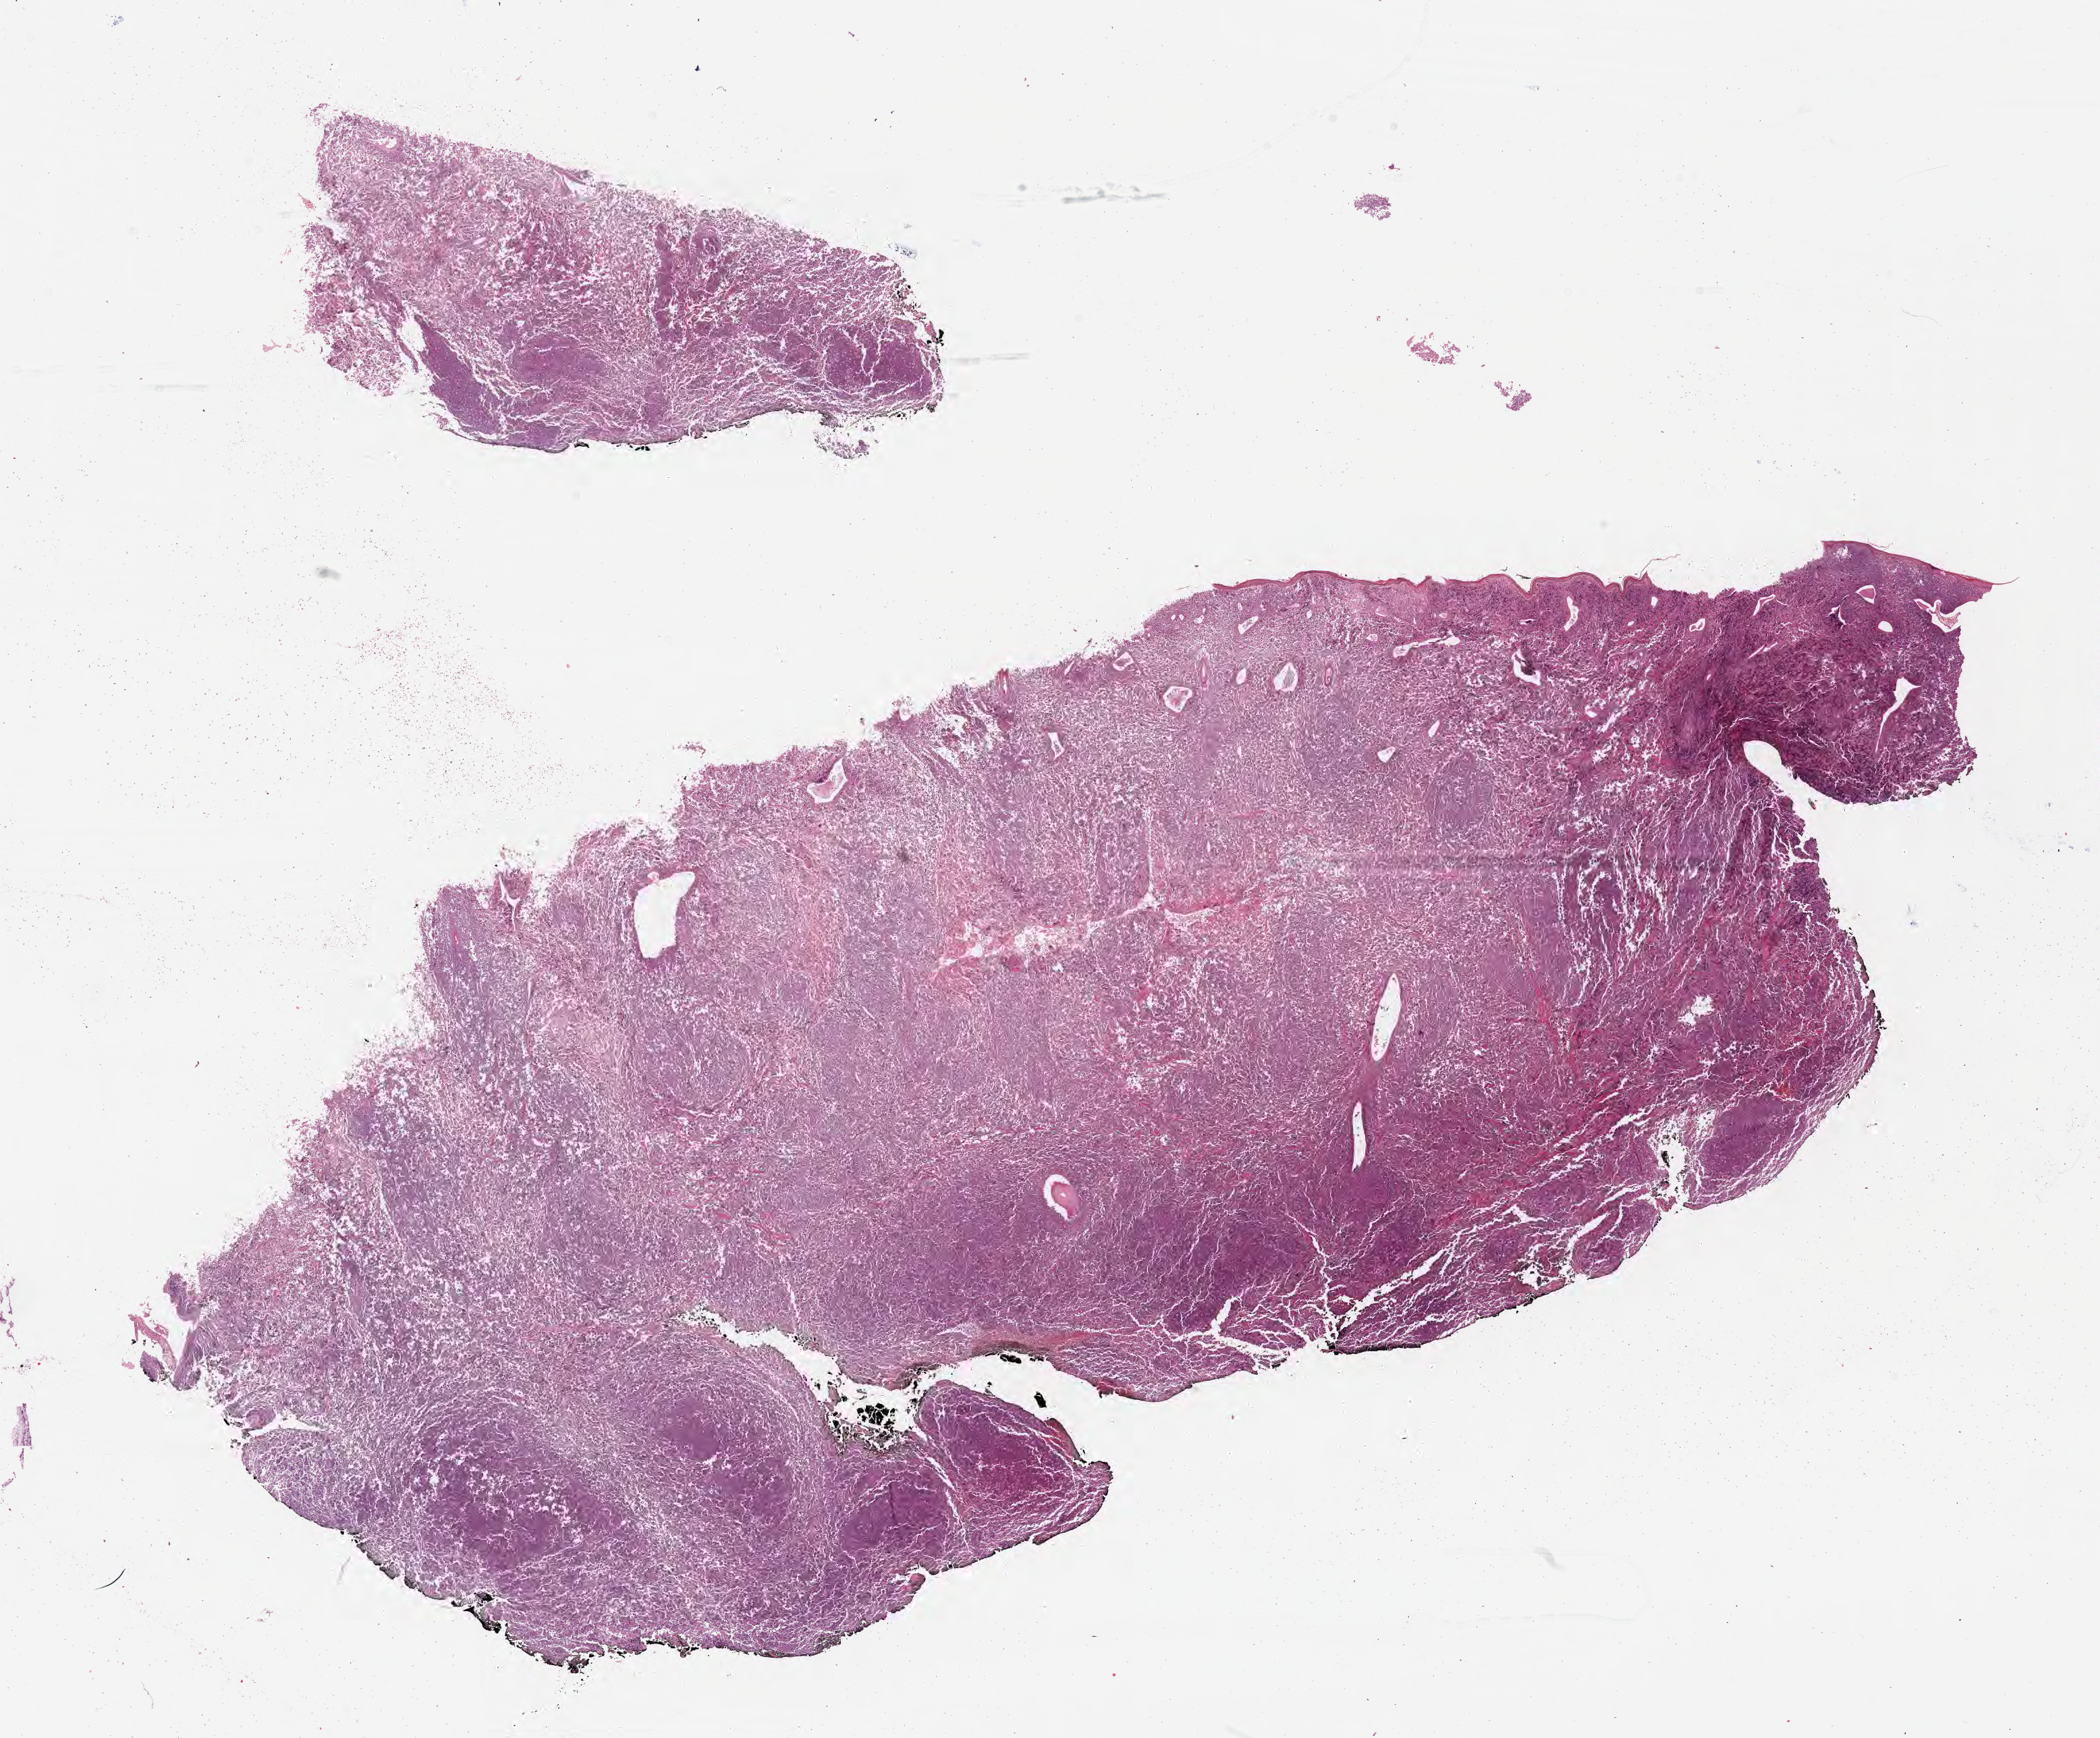
Whole-slide image, H&E stain, low-resolution overview of the scanned area, about 25.1 x 20.8 mm; FFPE section; specimen: primary tumor. Male patient, aged 46. Slide review estimates, as recorded: tumor cells 90%, tumor nuclei 95%, stromal cells 10%, necrosis 0%, normal cells 0%. Inflammatory infiltration, as recorded: lymphocyte infiltration 70%, monocyte infiltration 15%, neutrophil infiltration 5%.
Histologic diagnosis: Burkitt lymphoma, NOS. Ann Arbor stage (patient): Stage III. Section: bottom of the tissue portion.